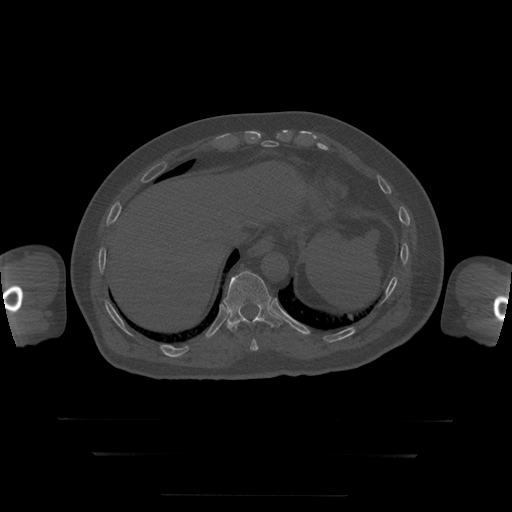
CT including the spine, one axial slice; slice 106 of 397 in the series (ordered by position); reconstruction kernel STANDARD; 120 kVp; bone window (W 1800 / L 400 HU); 512 × 512 image matrix, field of view 510 × 510 mm. Patient age 73 years. From the clinical record (not read from this slice): primary cancer: prostate.
Structures marked on this image (semi-automatically segmented with operator editing):
- T10 vertebra: bounding box (x1, y1, x2, y2) in pixels: (250, 339, 259, 351)
- T11 vertebra: (223, 271, 283, 332)